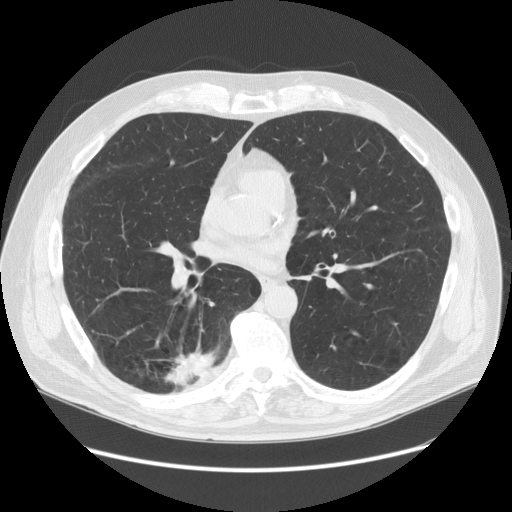
Low-dose screening chest CT, one axial slice. Position 73 of 149 along the scan axis. Reconstruction kernel STANDARD. Lung window (W 1500 / L -600 HU). 512 × 512 image matrix, field of view 400 × 400 mm.
Annotated regions visible in this slice (expert manual segmentation):
- lesion 1 (tumor, lower lobe of right lung): bounding box [x1, y1, x2, y2] px = [165, 346, 216, 386]